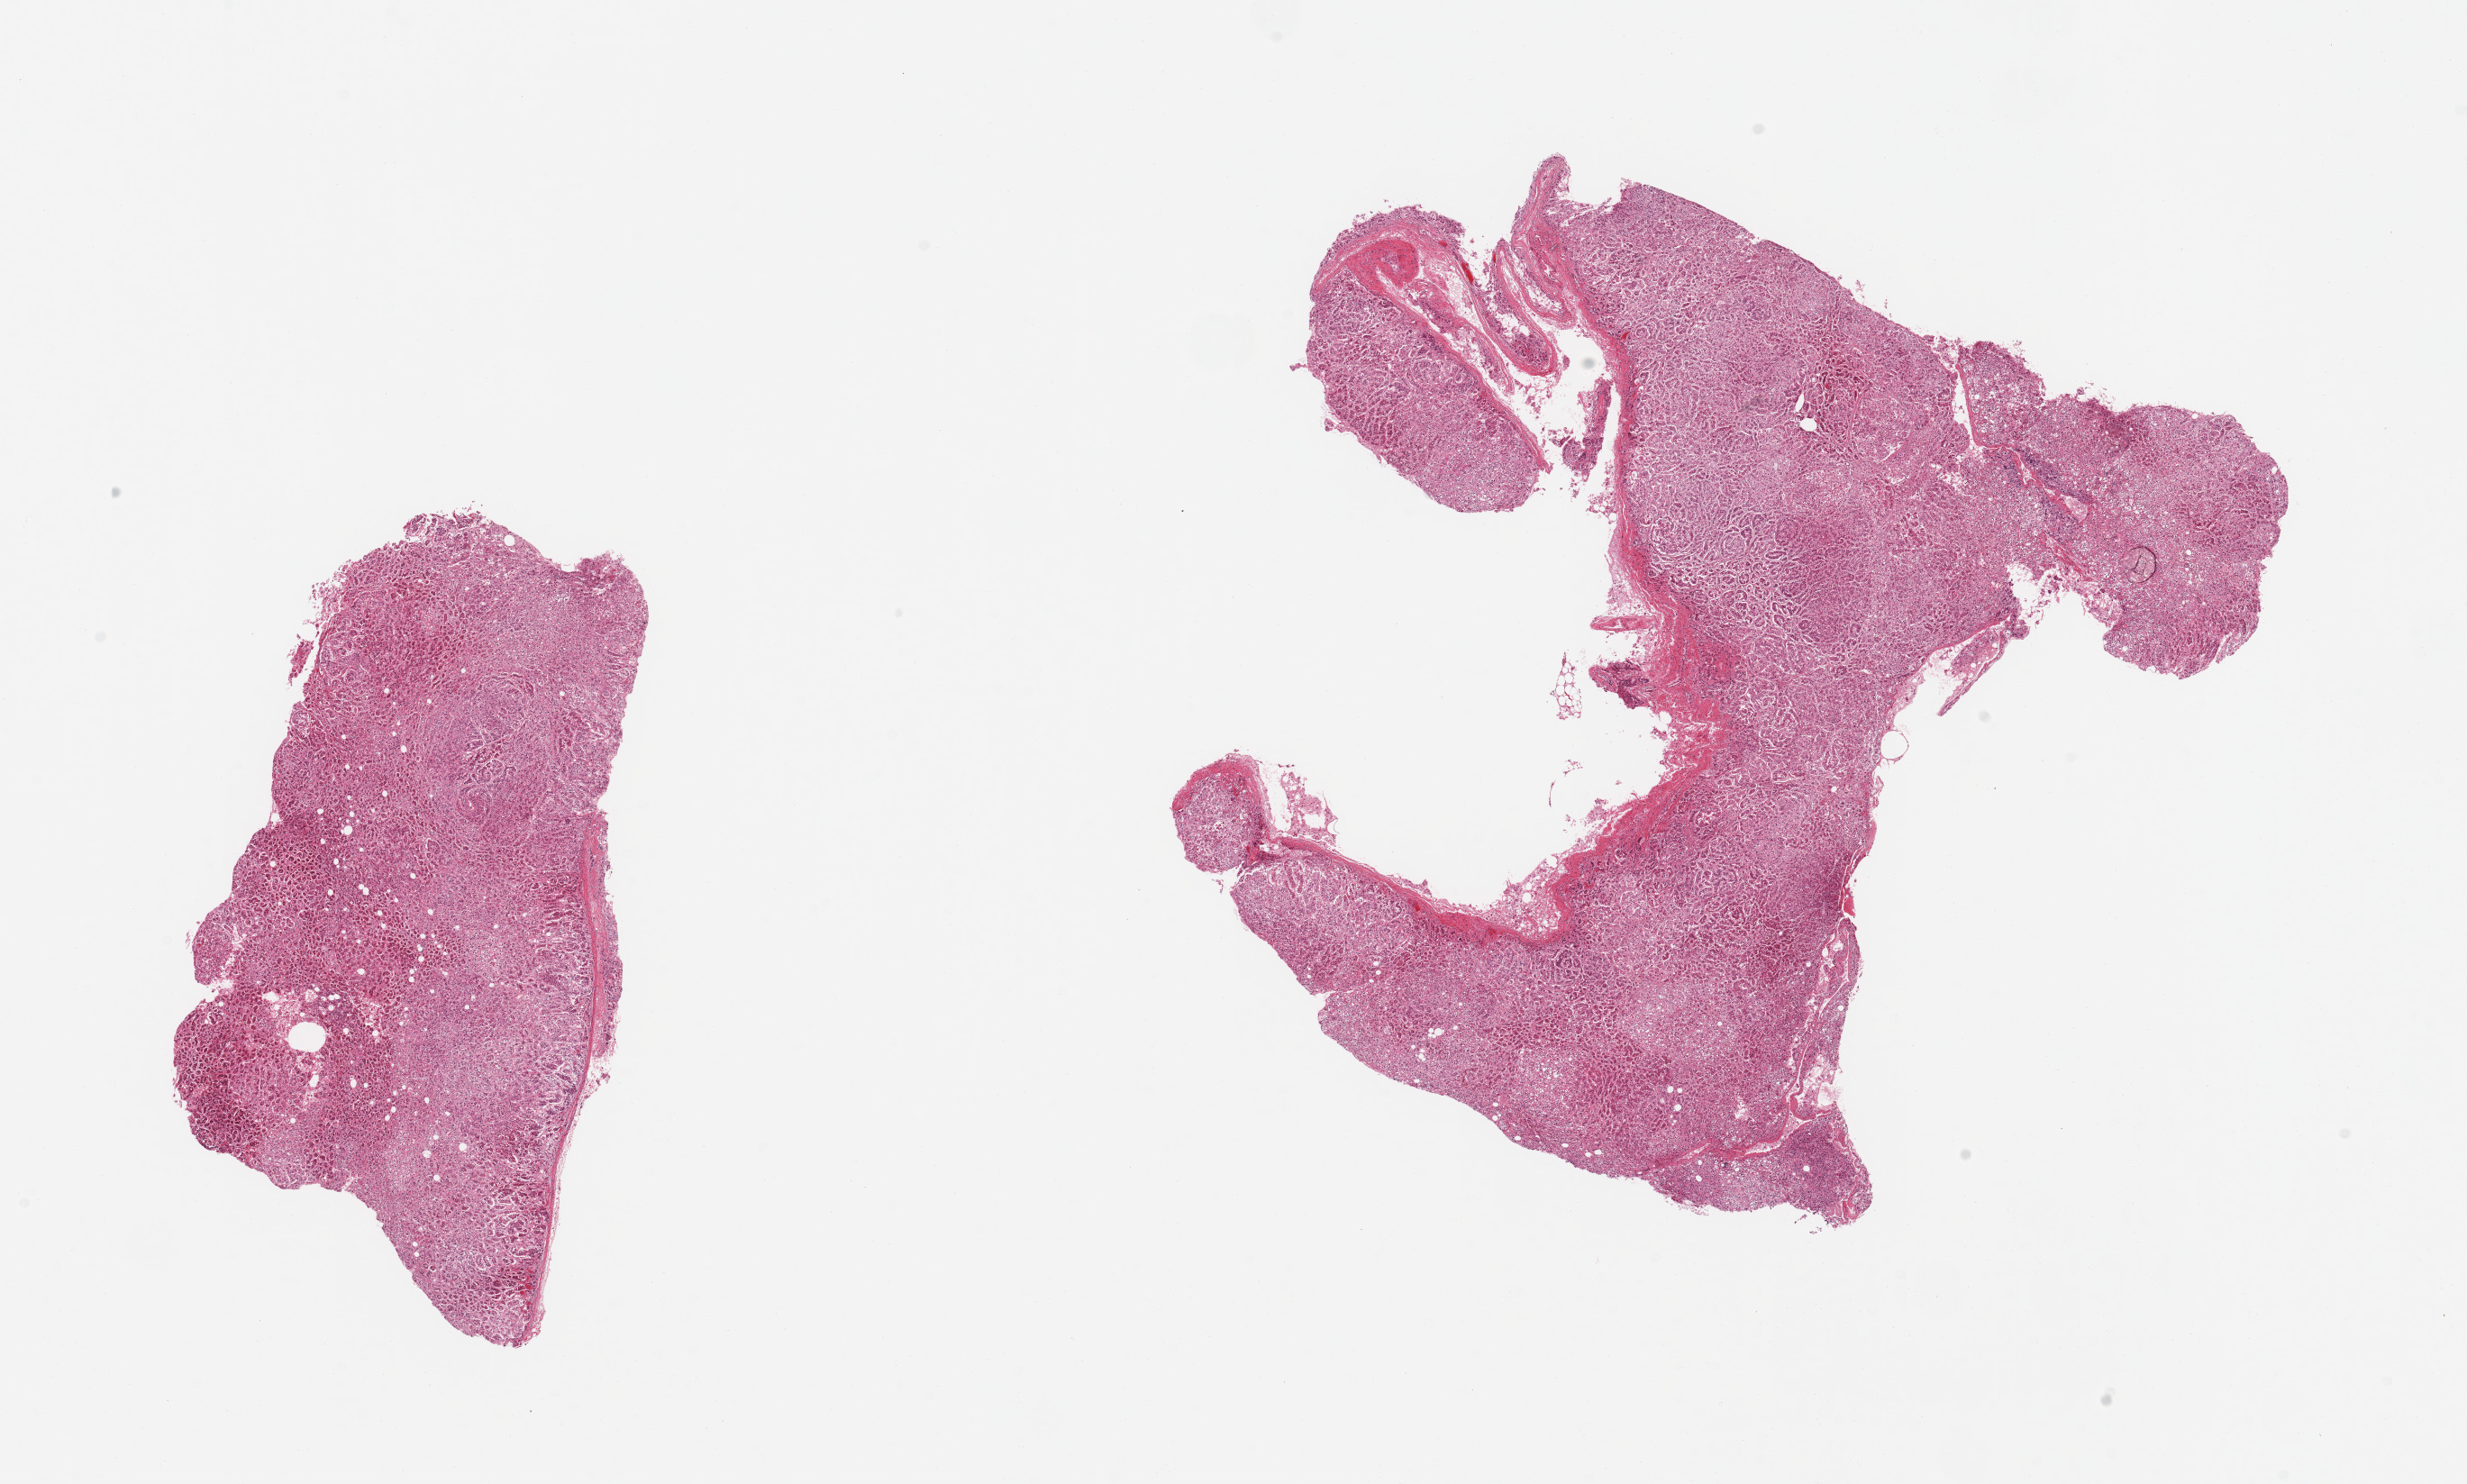
Digitized haematoxylin and eosin-stained section, low-resolution overview of the scanned area, about 21.7 x 13.0 mm (acquisition: 20x scan), PAXgene-fixed, paraffin-embedded tissue, sampled site (target tissue): adrenal gland, tissue donor sample. Donor: male.
Reviewer comment on this tissue sample: 2 pieces, cortex, moderately advanced autolysis.